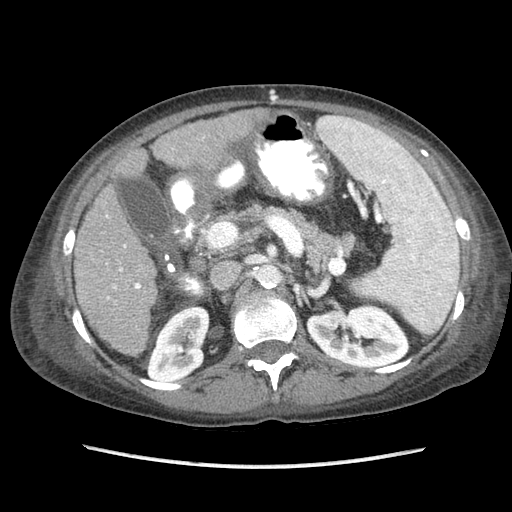
Contrast-enhanced abdominal CT (liver protocol), one axial slice; position 38 of 87 along the scan axis; 120 kVp; soft-tissue window (W 400 / L 40 HU); 512 × 512 image matrix, field of view 340 × 340 mm. From the clinical record (not read from this slice): diagnosis: hepatocellular carcinoma (patient treated with transarterial chemoembolisation; whether this scan precedes or follows treatment is not stated here); TNM stage (as recorded): Stage-IIIB; Child-Pugh class: A; tumour differentiation: no biopsy.
Annotated regions visible in this slice (semi-automatic segmentation, software-assisted and operator-edited):
- liver parenchyma outside the tumour (the mass and vessels are separate outlines, so this box may not span the whole liver): box from (x=74, y=108) to (x=268, y=354) px
- liver vessels: (x=106, y=215)–(x=141, y=299)